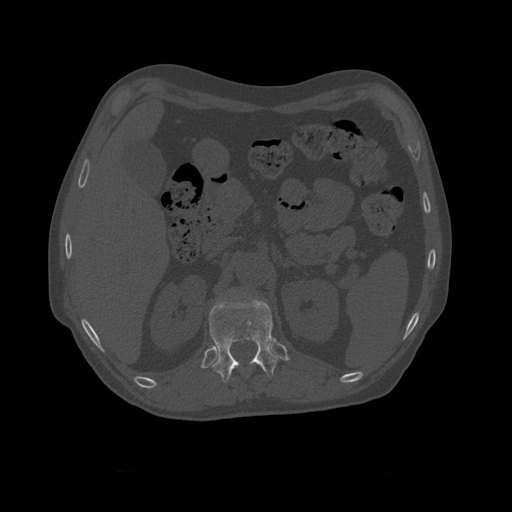
CT including the spine, one axial slice. Position 379 of 450 along the scan axis. Reconstruction kernel STANDARD. Bone window (W 1800 / L 400 HU). 1.25 mm slice thickness. 512 × 512 image matrix, field of view 405 × 405 mm. Patient age 75 years. Case-level facts recorded for this patient, not image findings: primary cancer: prostate.
Outlined on this slice (semi-automatic segmentation, software-assisted and operator-edited):
- T11 vertebra: bounding box [x1, y1, x2, y2] px = [209, 297, 282, 383]